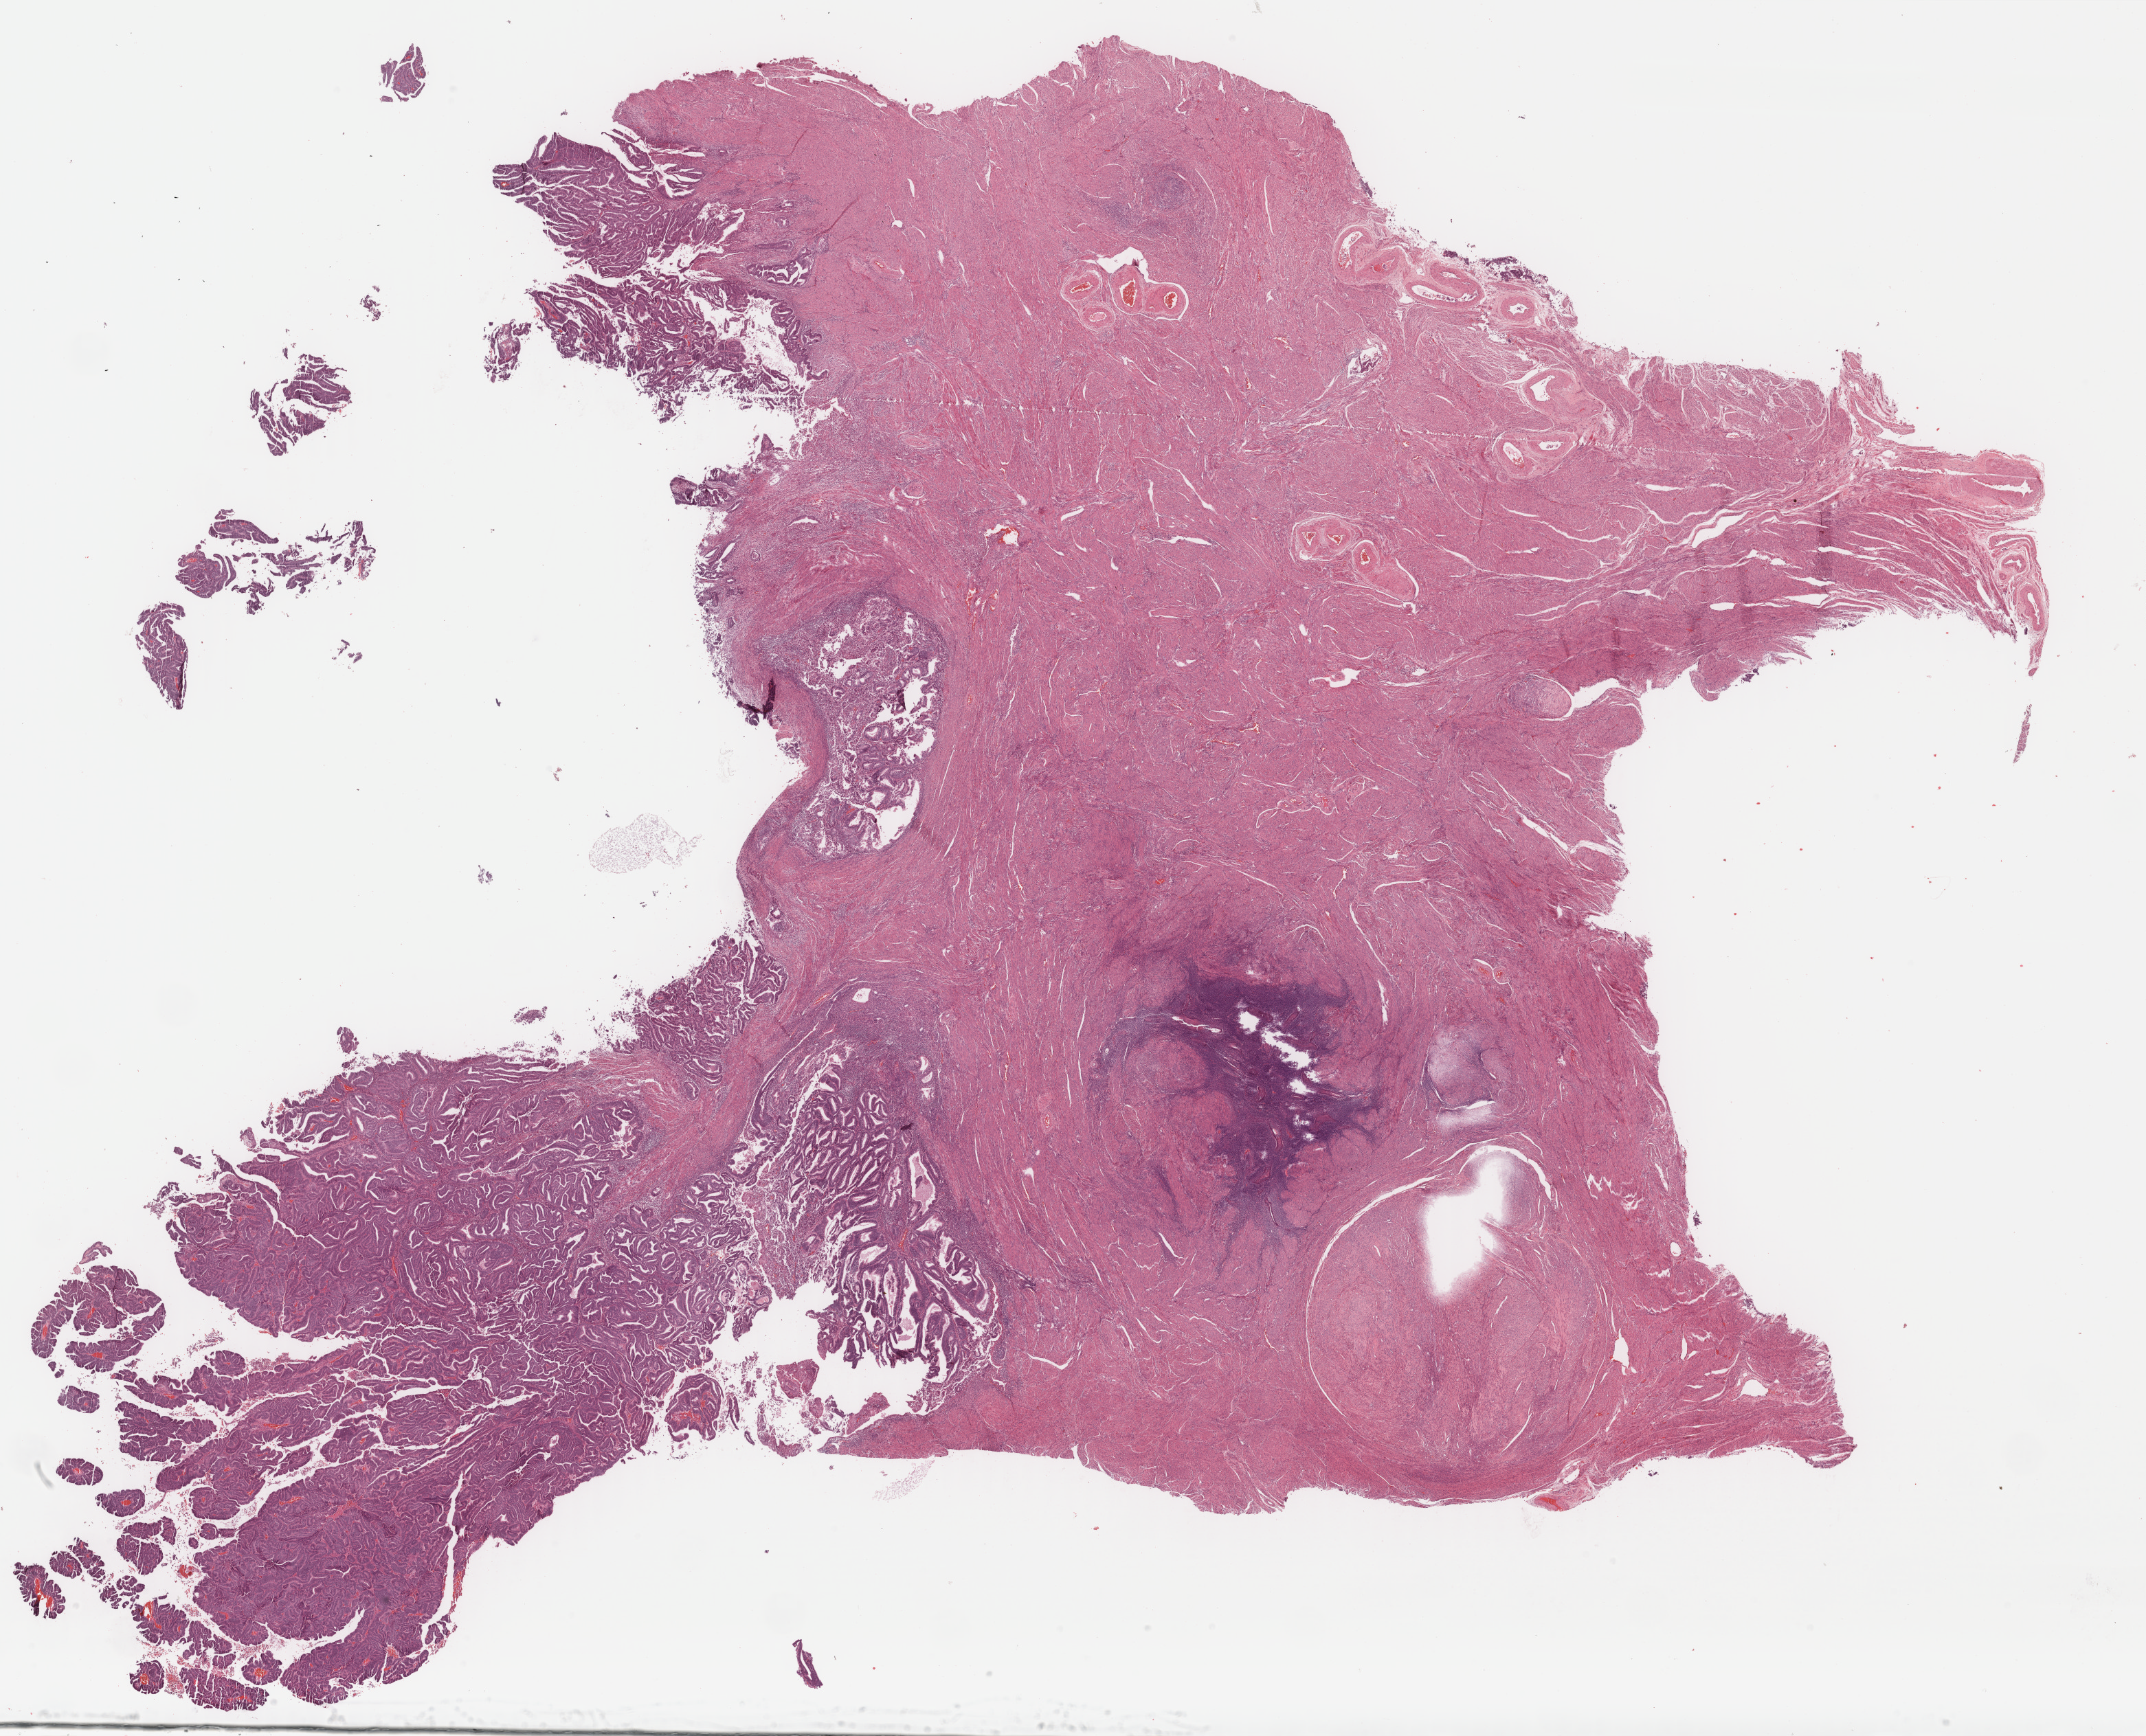
Hematoxylin and eosin (H&E) stained whole-slide image, shown as a low-resolution overview of the whole scanned area (about 24.8 x 20.1 mm). Formalin-fixed paraffin-embedded (FFPE) diagnostic section. Sample: primary tumour, uterus. Patient: female, age at initial diagnosis 55 years. Histologic grade: G1 (well differentiated).
Diagnosis: Endometrioid adenocarcinoma, NOS (endometrium). FIGO stage: IIIC. Lymph nodes positive (case pathology): 3 of 4 examined.